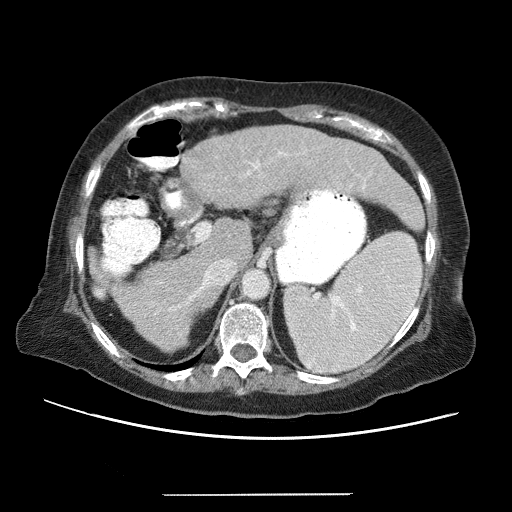
Contrast-enhanced abdominal CT (liver protocol), one axial slice. Slice 38 of 65 in the series (ordered by position). Reconstruction kernel STANDARD. 120 kVp. Soft-tissue window (W 400 / L 40 HU). 2.5 mm slice thickness. 512 × 512 image matrix, field of view 380 × 380 mm. From the clinical record (not read from this slice): diagnosis: hepatocellular carcinoma (patient treated with transarterial chemoembolisation; whether this scan precedes or follows treatment is not stated here); TNM stage (as recorded): Stage-IIIB; Child-Pugh class: A.
Structures marked on this image (semi-automatic segmentation, software-assisted and operator-edited):
- liver parenchyma outside the tumour (the mass and vessels are separate outlines, so this box may not span the whole liver): bounding box <88,124,416,352> (left, top, right, bottom; pixels)
- liver vessels: <108,136,404,340>